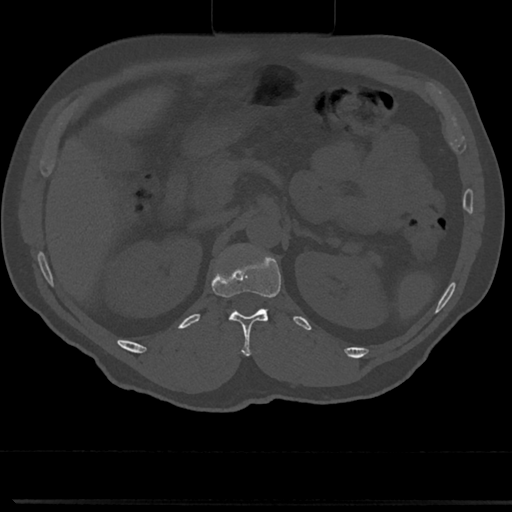
CT including the spine, one axial slice. 120 kVp. Bone window (W 1800 / L 400 HU). 512 × 512 image matrix, field of view 355 × 355 mm. Patient: male, 61 years. Case-level facts recorded for this patient, not image findings: primary cancer: prostate.
Annotated regions visible in this slice (semi-automatic segmentation, software-assisted and operator-edited):
- L1 vertebra: bounding box (x1, y1, x2, y2) in pixels: (219, 243, 255, 315)
- T12 vertebra: (226, 269, 282, 357)